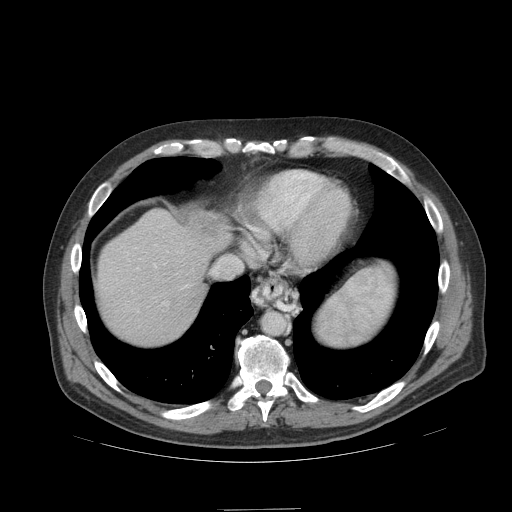
Contrast-enhanced abdominal CT (liver protocol), one axial slice. Position 89 of 99 along the scan axis. Soft-tissue window (W 400 / L 40 HU). 2.5 mm slice thickness. 512 × 512 image matrix. Case-level facts recorded for this patient, not image findings: diagnosis: hepatocellular carcinoma (patient treated with transarterial chemoembolisation; whether this scan precedes or follows treatment is not stated here); TNM stage (as recorded): Stage-I; Child-Pugh class: A; tumour nodularity: uninodular; tumour size: 3.6 cm.
Structures marked on this image (semi-automatically segmented with operator editing):
- abdominal aorta: bounding box [x1, y1, x2, y2] px = [263, 314, 285, 334]
- liver parenchyma outside the tumour (the mass and vessels are separate outlines, so this box may not span the whole liver): [98, 209, 230, 344]
- mass: [191, 213, 219, 246]
- liver vessels: [154, 264, 187, 287]